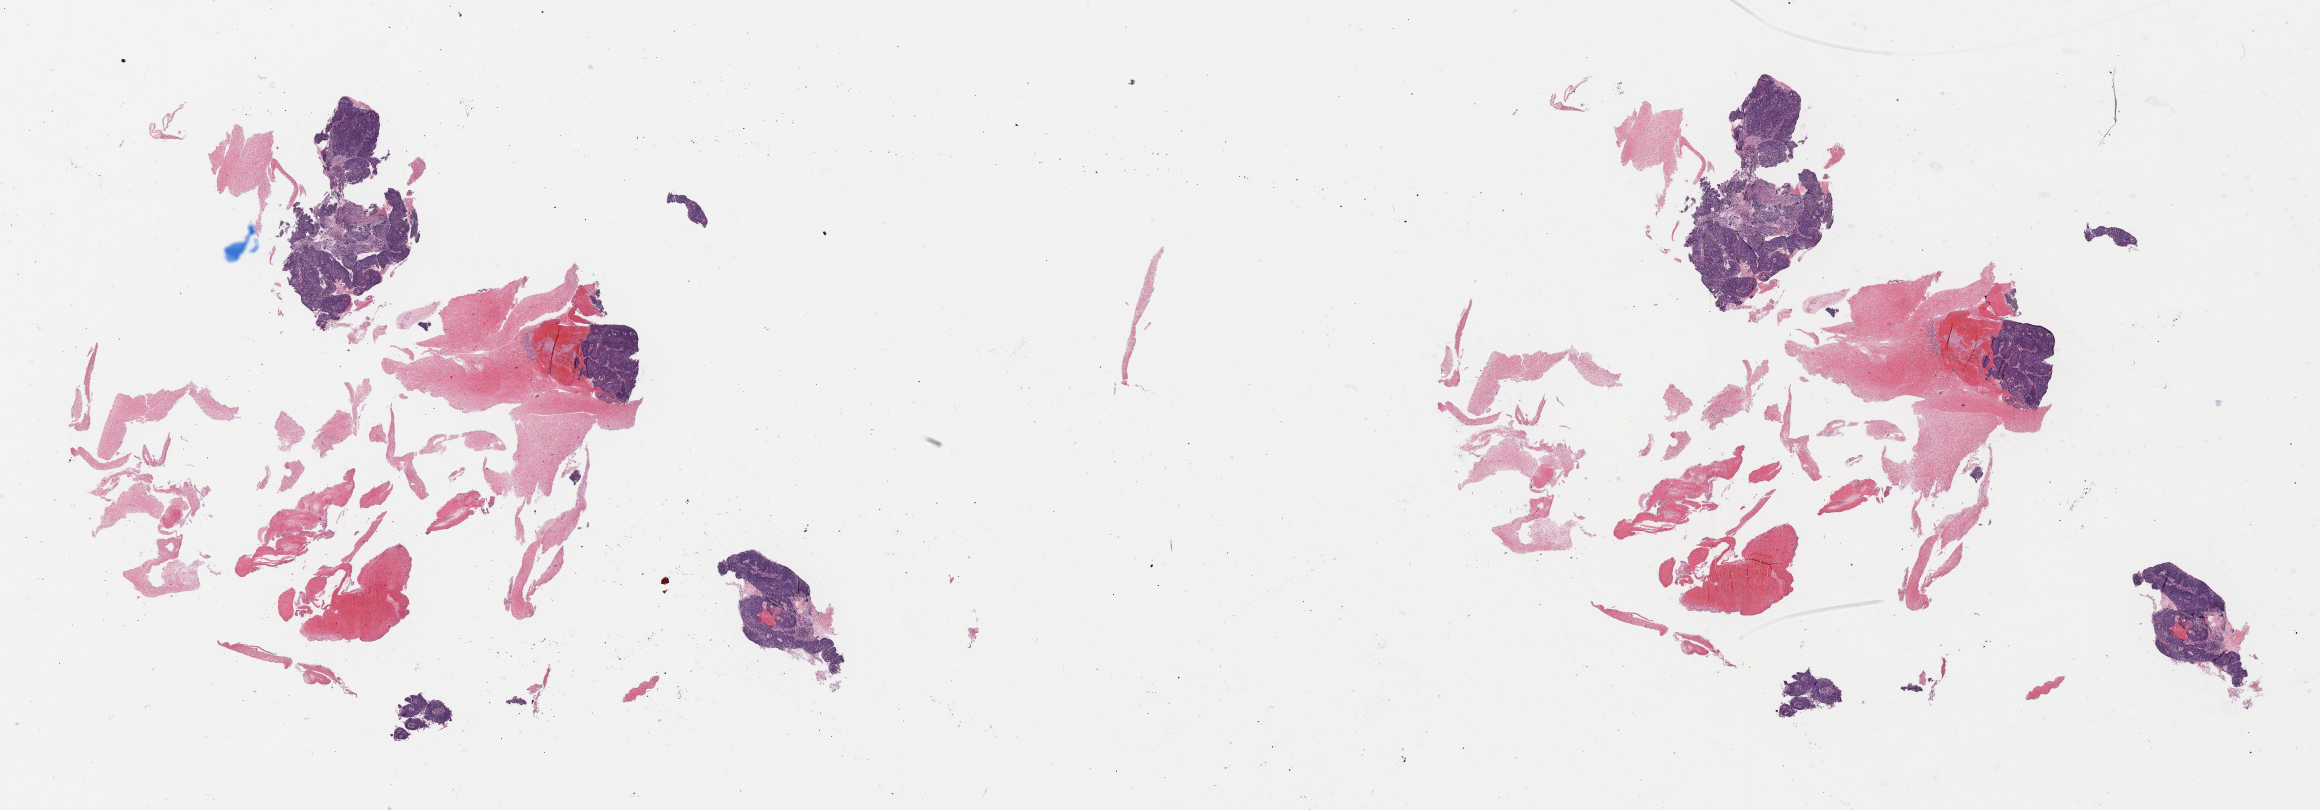
Digitized H&E-stained tissue section (whole slide), whole scanned area (about 36.6 x 12.8 mm, slide scanned at 40x) shown as a low-resolution overview, formalin-fixed paraffin-embedded (FFPE) diagnostic section, cervix, primary tumour sample. Female, age 43 years at initial diagnosis. Histologic grade: G3 (poorly differentiated).
Diagnosis: Papillary squamous cell carcinoma (cervix uteri). FIGO stage: IB2.